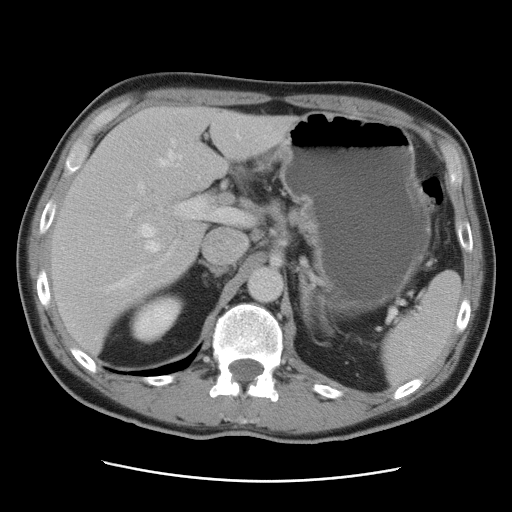
Contrast-enhanced abdominal CT, one axial slice. Slice 57 of 89 in the series (ordered by position). Soft-tissue window (W 400 / L 40 HU). 5 mm slice thickness. 512 × 512 image matrix, field of view 366 × 366 mm. Male patient, age 59 years. Case-level facts recorded for this patient, not image findings: diagnosis: colorectal cancer liver metastases, imaged before liver resection; multiple liver metastases: yes; largest metastasis: 0.6 cm; disease in both lobes: yes.
Outlined on this slice (outlined manually by an expert reader):
- hepatic veins: box from (x=105, y=135) to (x=240, y=293) px
- liver: (x=52, y=106)–(x=294, y=354)
- planned liver remnant (the part of the liver to remain after resection): (x=75, y=107)–(x=242, y=237)
- portal vein (with intrahepatic branches): (x=127, y=183)–(x=244, y=270)